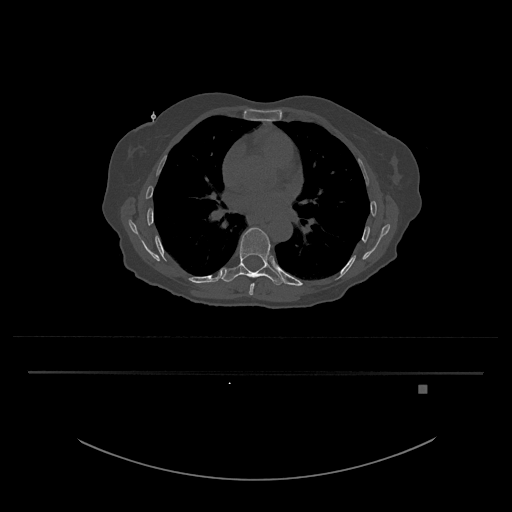
CT including the spine, one axial slice; position 768 of 797 along the scan axis; reconstruction kernel Br40s/3; bone window (W 1800 / L 400 HU); 512 × 512 image matrix. Female patient, age 57 years. From the clinical record (not read from this slice): primary cancer: cervical.
Outlined on this slice (semi-automatically segmented with operator editing):
- T8 vertebra: box from (x=249, y=283) to (x=255, y=296) px
- T9 vertebra: (x=222, y=227)–(x=285, y=285)